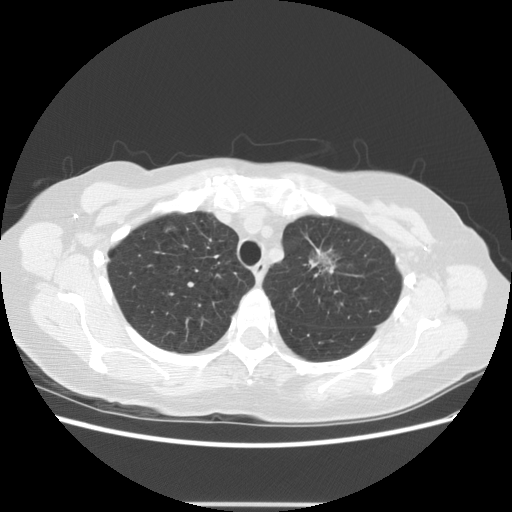
Chest CT (low-dose screening protocol), one axial image. Third screening round (two years after baseline). Lung window (W 1500 / L -600 HU). 2.5 mm slice thickness. 512 × 512 image matrix, field of view 360 × 360 mm. Female, age 65 years at enrolment. Former smoker at enrolment.
Expert-annotated lung lesion, bounding box [x1, y1, x2, y2] px = [291, 226, 369, 294]. The exam's reader record, not a measurement of the box and not confirmed to be the same lesion: non-calcified nodule or mass ≥4 mm, left upper lobe, 17 × 14 mm, poorly defined margins, ground glass attenuation, pre-existing on the prior screen: yes; interval growth: yes. Official screen result: positive, other. Later outcome: lung cancer diagnosed 96 days after this screen — adenocarcinoma, NOS, left upper lobe, moderately differentiated (G2), stage IA (AJCC 6th edition), 30 mm at pathology.